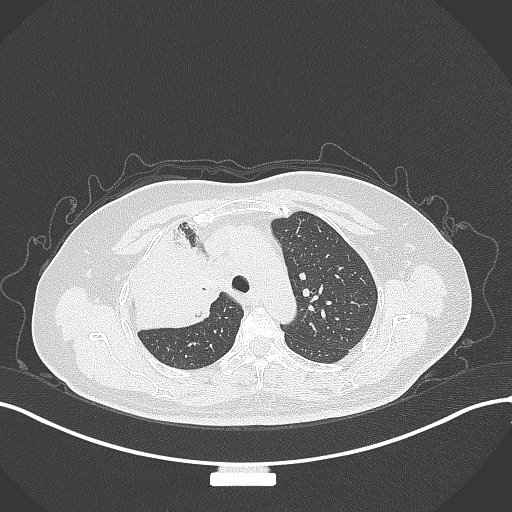
Chest CT, one axial slice. Position 227 of 309 along the scan axis. 120 kVp. Lung window (W 1500 / L -600 HU). 512 × 512 image matrix. Patient: female, 60 years. From the clinical record (not read from this slice): clinical TNM (as recorded): T3 N1 M1.
Annotated regions visible in this slice (rectangle marked by the reading radiologist):
- lung tumour (recorded histology: adenocarcinoma): box from (x=124, y=225) to (x=222, y=343) px